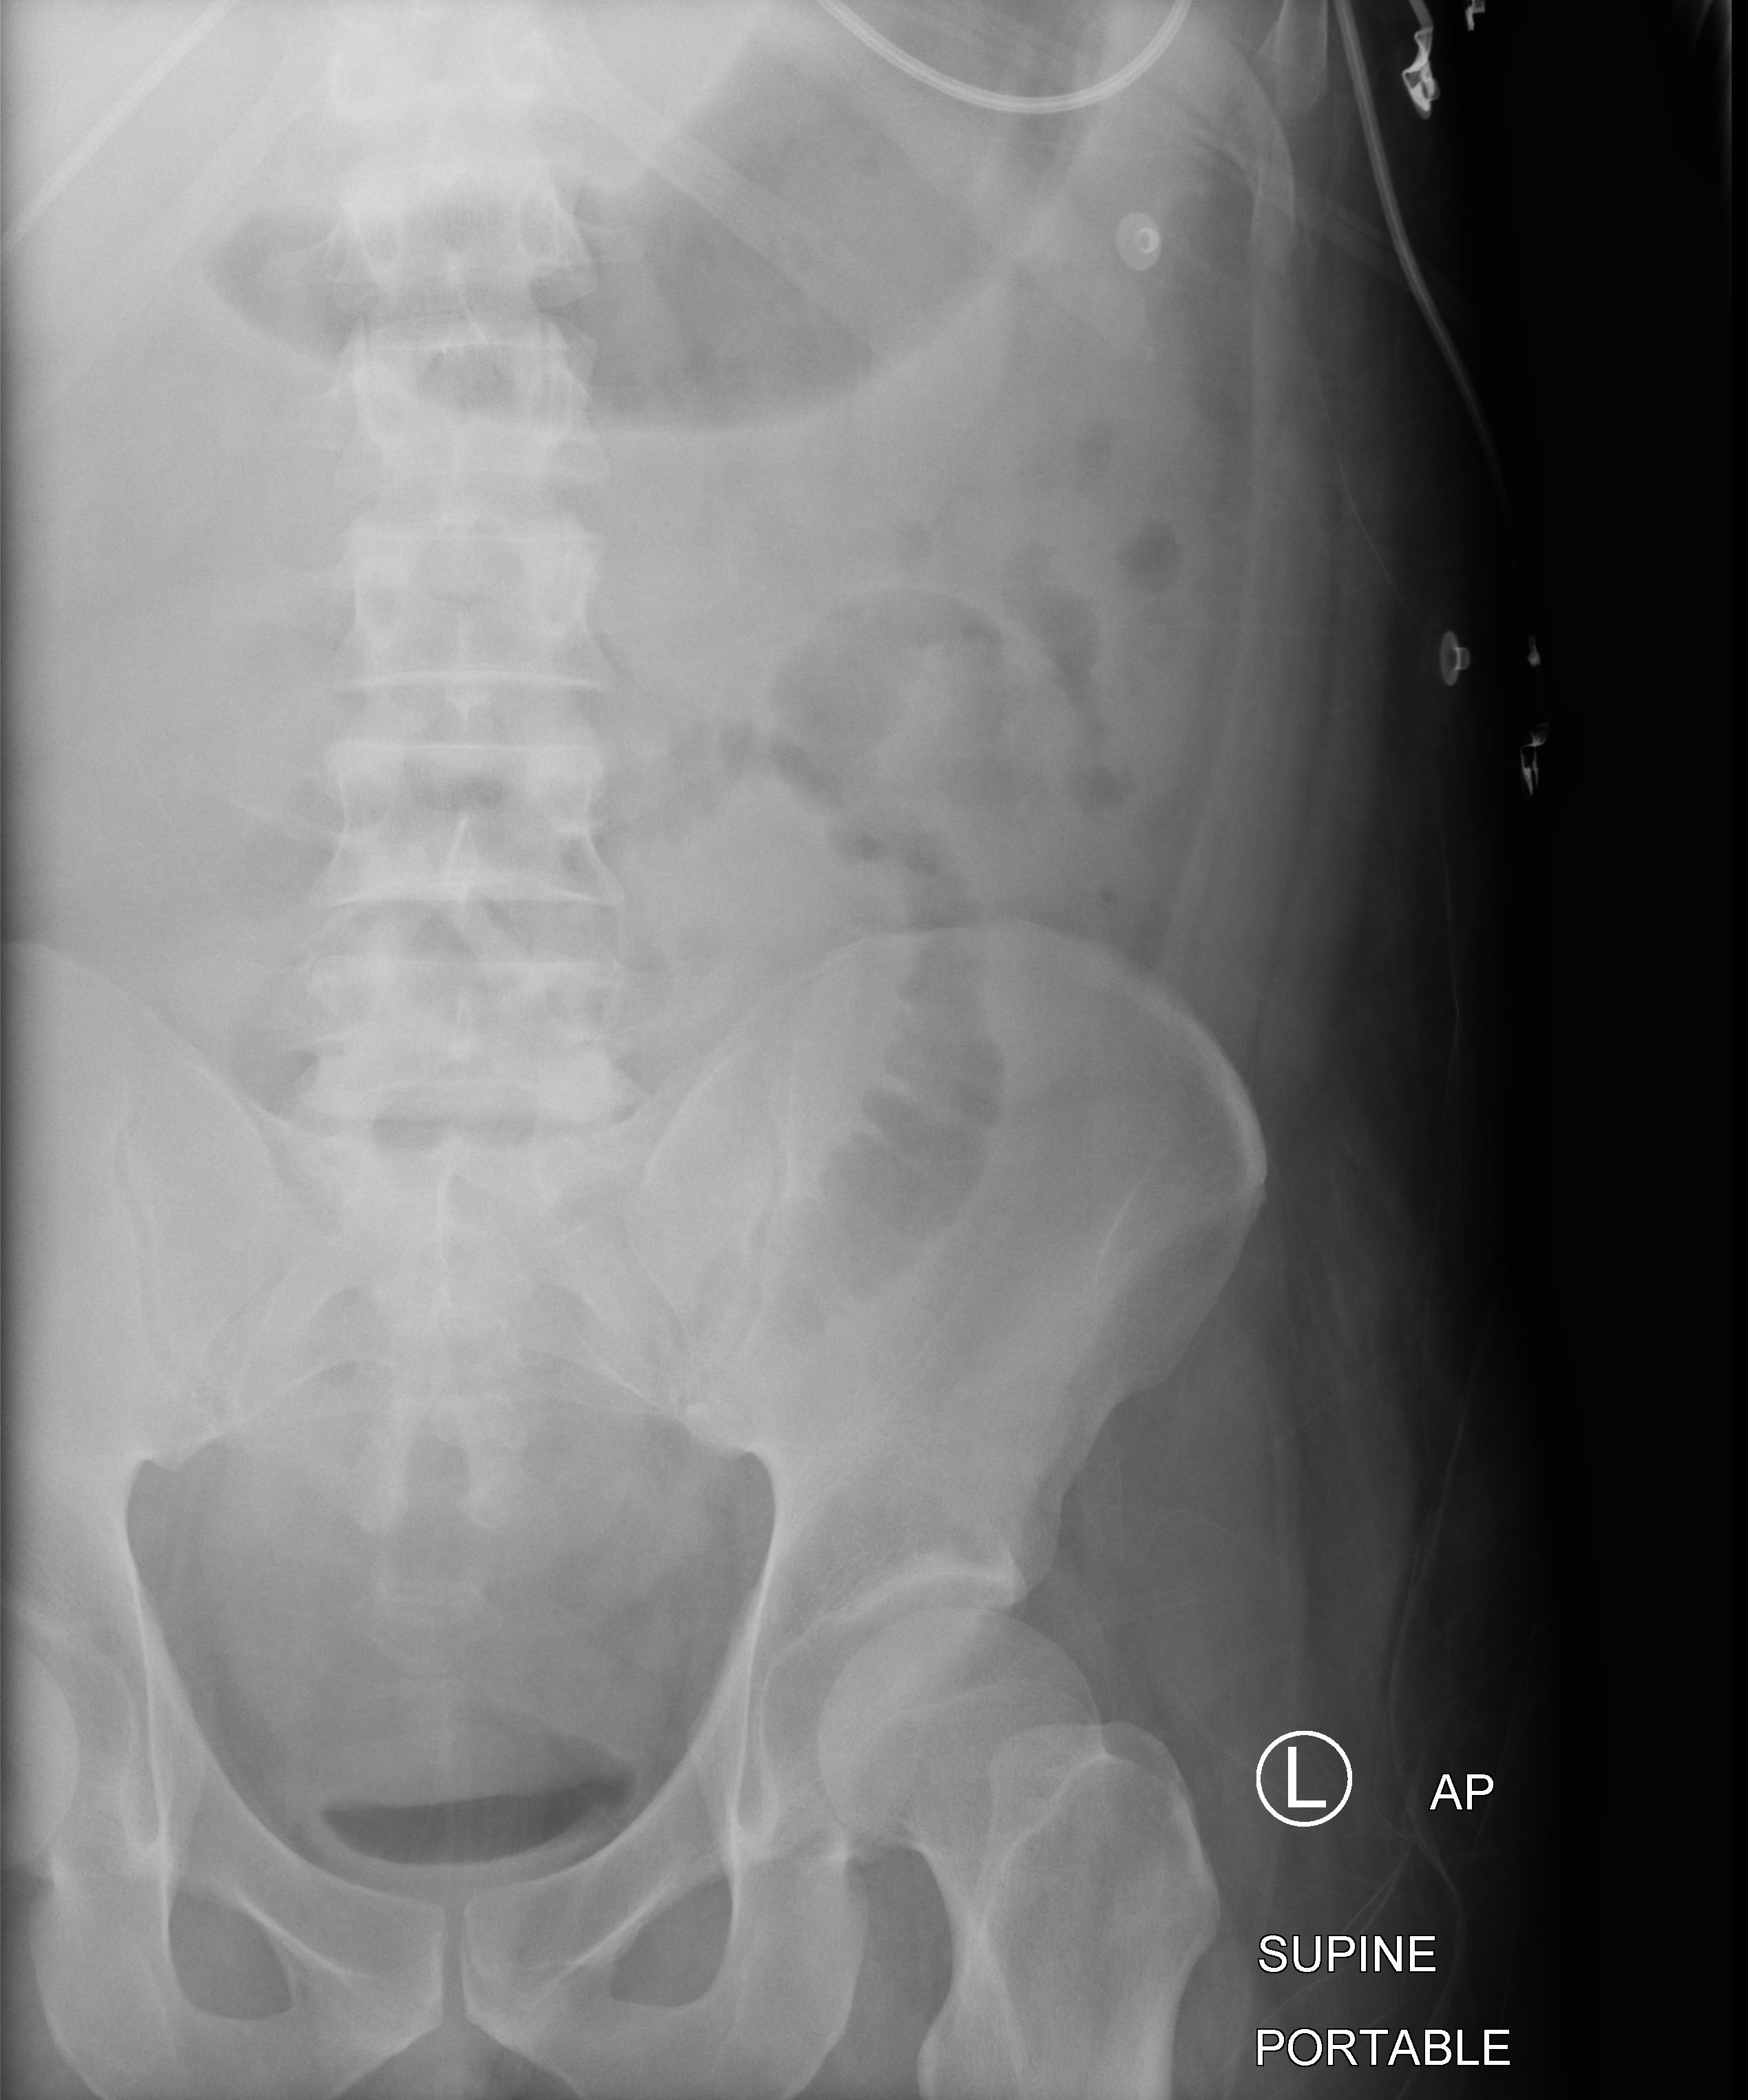
Bedside abdomen radiograph (computed radiography); anteroposterior (AP) projection. Male patient hospitalised with COVID-19, age 18–59 years.
Hospital-stay facts (about this admission, not read from this image; timing relative to this image not recorded):
- diabetes (admission record): no